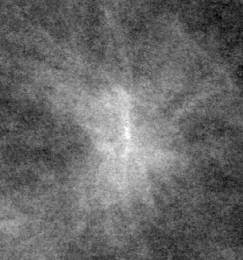
Crop from a digitized film mammogram around one marked abnormality; left breast; CC view.
- Finding: mass, shape irregular / architectural distortion, margins spiculated; BI-RADS assessment category 4; pathology result (as recorded, not read from the image): malignant.